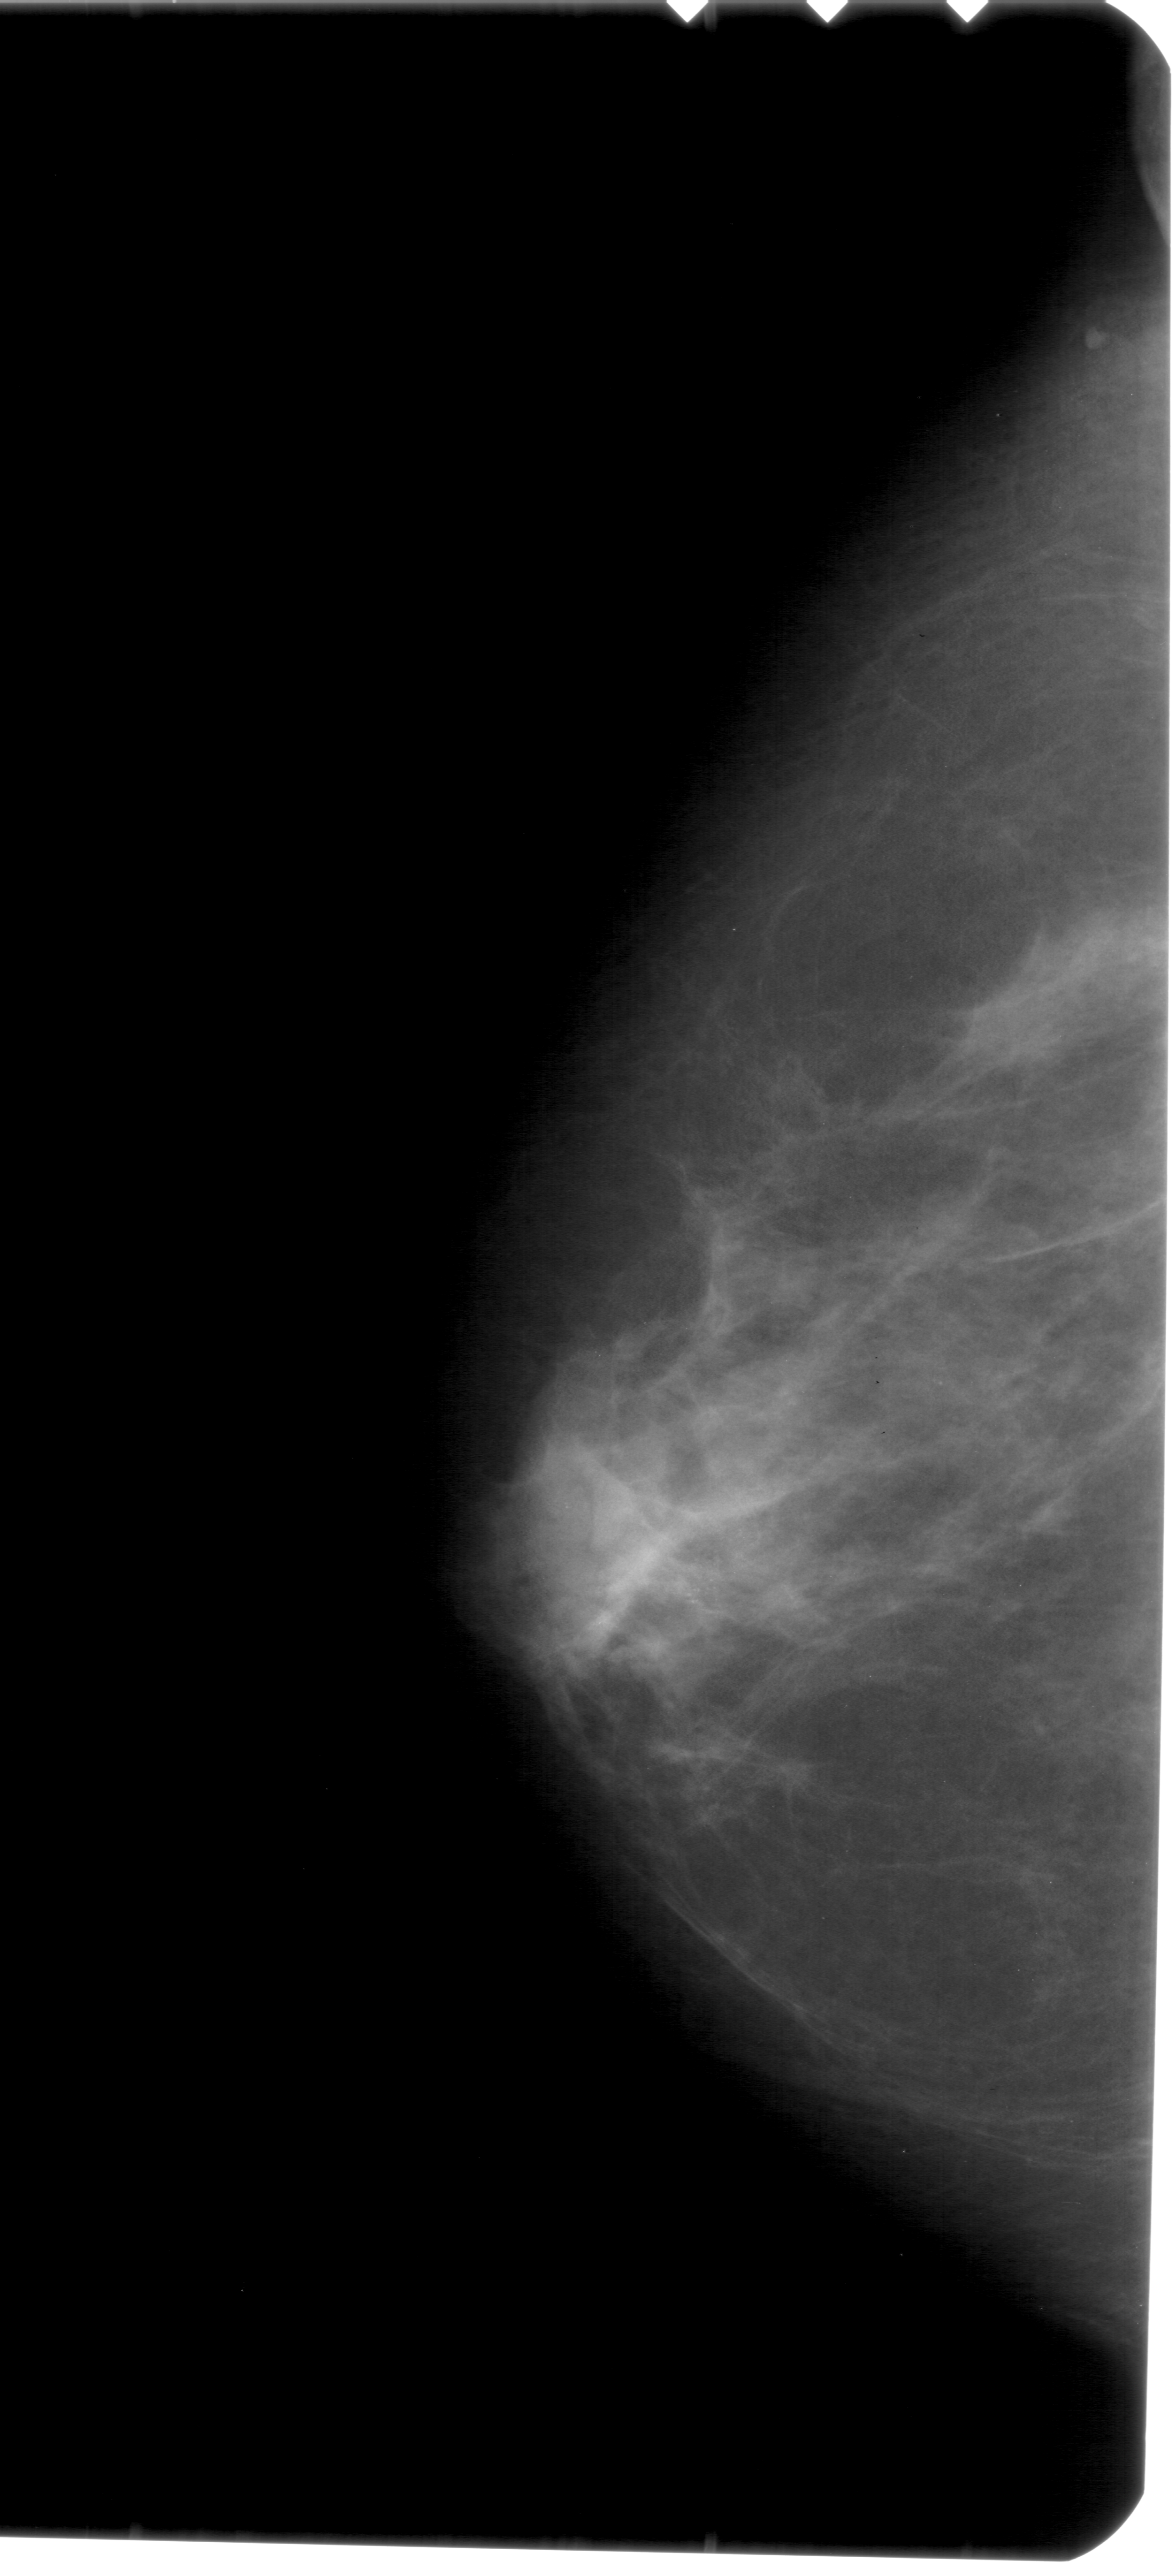
Digitized screen-film mammogram; left breast; CC view; breast composition: scattered fibroglandular densities (BI-RADS density category 2 of 4).
- Calcifications, morphology pleomorphic, distribution clustered; BI-RADS assessment category 4; pathology result (as recorded, not read from the image): benign.